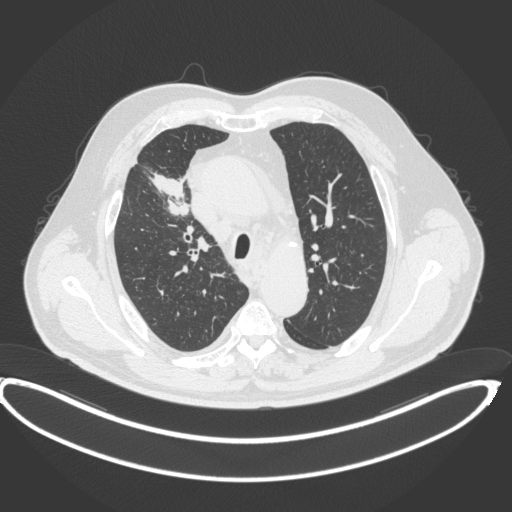
Chest CT, one axial slice; slice 292 of 395 in the series (ordered by position); 120 kVp; lung window (W 1500 / L -600 HU); 1 mm slice thickness; 512 × 512 image matrix, field of view 448 × 448 mm. Patient: male, 62 years. From the clinical record (not read from this slice): clinical TNM (as recorded): T1c N3 M1c.
Outlined on this slice (bounding box drawn by a radiologist):
- lung tumour (recorded histology: adenocarcinoma): bounding box <147,169,190,220> (left, top, right, bottom; pixels)